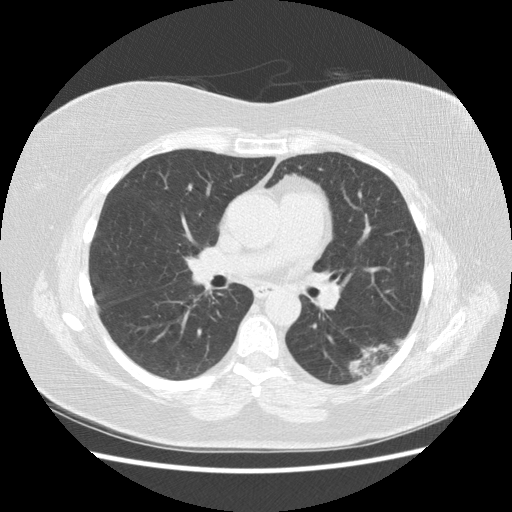
Low-dose screening chest CT, one axial slice. Position 85 of 151 along the scan axis. 120 kVp. Lung window (W 1500 / L -600 HU). 2.5 mm slice thickness. 512 × 512 image matrix.
Annotated regions visible in this slice (outlined manually by an expert reader):
- lesion 1 (tumor, lower lobe of left lung): bounding box <349,338,404,378> (left, top, right, bottom; pixels)